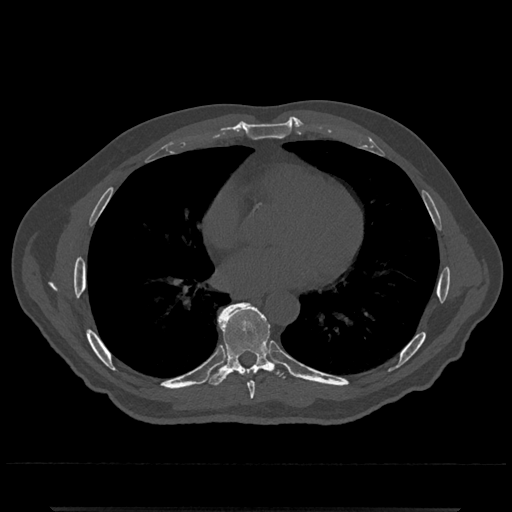
CT including the spine, one axial slice. Slice 686 of 797 in the series (ordered by position). Reconstruction kernel Br40s/3. Bone window (W 1800 / L 400 HU). 0.5 mm slice thickness. 512 × 512 image matrix, field of view 393 × 393 mm. Patient: male, 67 years. Case-level facts recorded for this patient, not image findings: primary cancer: prostate.
Structures marked on this image (semi-automatic segmentation, software-assisted and operator-edited):
- T7 vertebra: bounding box <248,382,255,400> (left, top, right, bottom; pixels)
- T8 vertebra: <204,303,291,387>